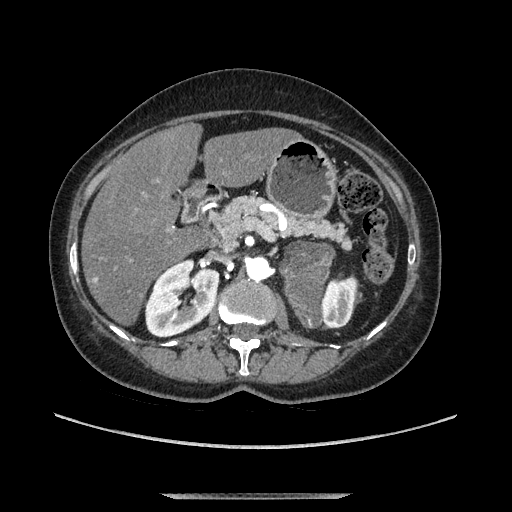
Contrast-enhanced abdominal CT, one axial slice. Position 64 of 169 along the scan axis. Soft-tissue window (W 400 / L 40 HU). 1.25 mm slice thickness. 512 × 512 image matrix. Female patient. From the clinical record (not read from this slice): diagnosis: adrenocortical carcinoma; tumour side: left adrenal; tumour size at pathology: 9 cm.
Structures marked on this image (semi-automatic segmentation, software-assisted and operator-edited):
- mass: bounding box <286,245,333,328> (left, top, right, bottom; pixels)